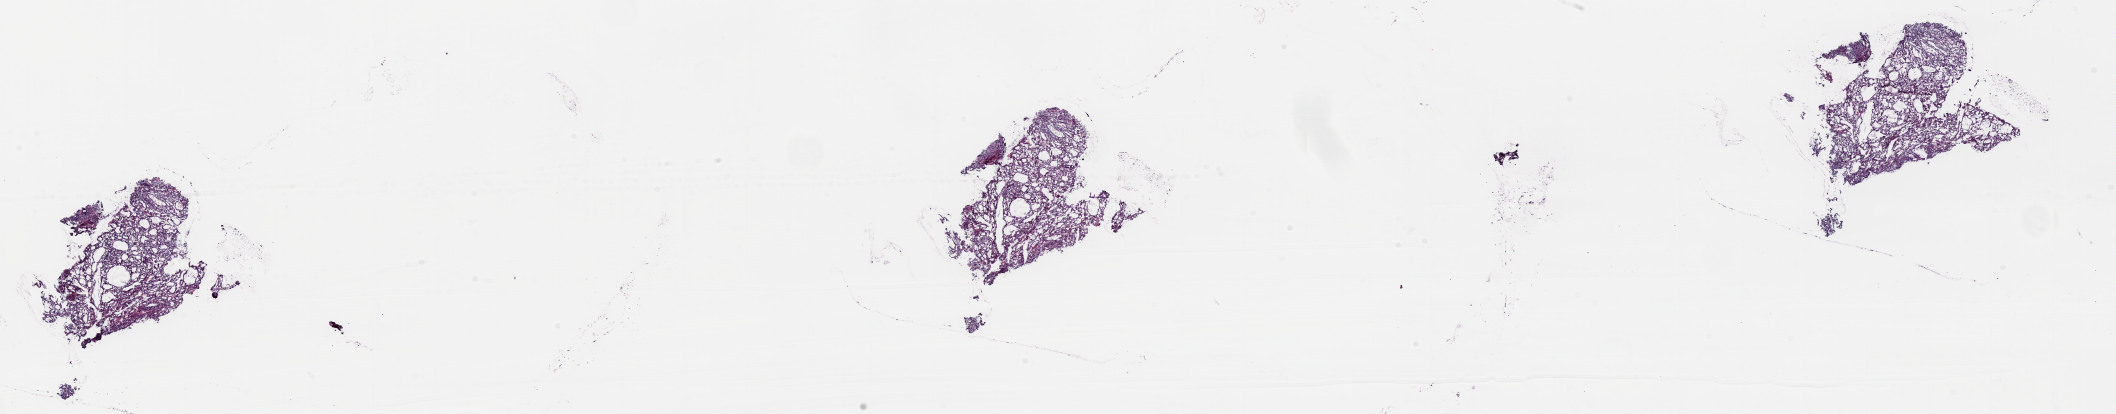
Whole-slide histology image, H&E-stained, low-resolution overview of the scanned area, about 33.5 x 6.5 mm (slide scanned at 20x). Frozen section from the top of the tissue portion. Solid tissue normal (non-tumour tissue) sample from the thyroid. Patient: female, age at initial diagnosis 53 years. Slide review estimates, as recorded: tumour cells 0%, tumour nuclei 0%, normal cells 100%, stromal cells 0%, necrosis 0%. Infiltration values recorded for this section: lymphocyte infiltration 0%, monocyte infiltration 0%, neutrophil infiltration 0%.
This section: solid tissue normal sample (biorepository sample class). Patient diagnosis: Papillary adenocarcinoma, NOS (thyroid gland).